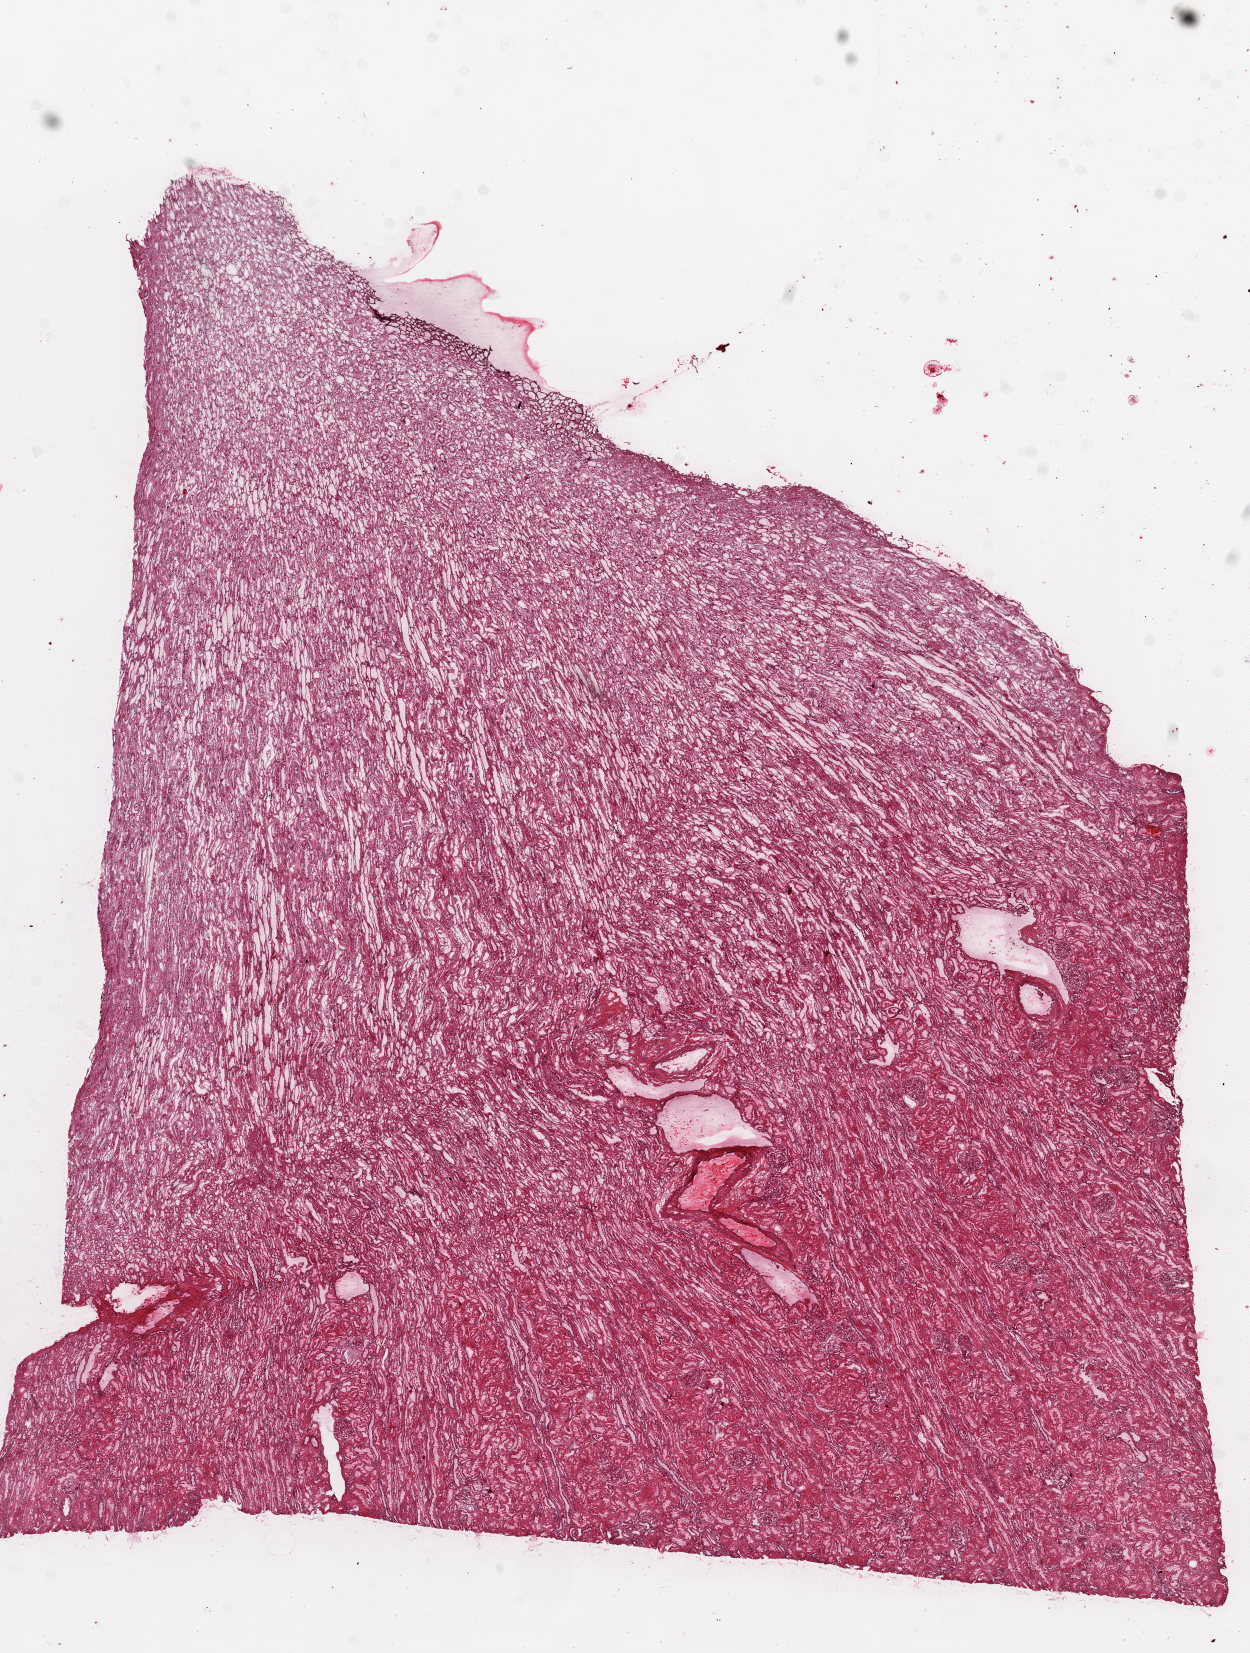
Digitized H&E-stained tissue section (whole slide), low-resolution overview of the scanned area, about 10.0 x 13.3 mm (from a 20x scan). Frozen section from the top of the tissue portion. Solid tissue normal (non-tumour tissue) sample from the kidney. Patient: male, age at initial diagnosis 40 years.
* this section: solid tissue normal (non-tumour) sample from the same patient
* patient diagnosis: Clear cell adenocarcinoma, NOS